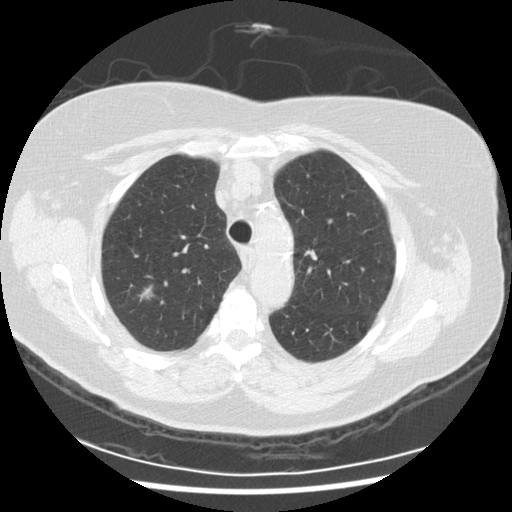
Chest CT (low-dose screening protocol), one axial image; third screening round (two years after baseline); lung window (W 1500 / L -600 HU); 2.5 mm slice thickness; standard (soft-tissue) reconstruction kernel (STANDARD); slice 56 of 254 in the series. Female participant, aged 72 years at enrolment. Current smoker at enrolment.
Expert reader's lesion annotation, bounding box <130,279,163,309> (left, top, right, bottom; pixels). The exam's reader record, not a measurement of the box and not confirmed to be the same lesion: non-calcified nodule or mass ≥4 mm, right upper lobe, 9 × 8 mm, poorly defined margins, ground glass attenuation, pre-existing on the prior screen: no. Official screen result: positive, other. Lung cancer was diagnosed 121 days after this screen: squamous cell carcinoma, NOS, right upper lobe, poorly differentiated (G3), stage IIIA (AJCC 6th edition), 22 mm at pathology.